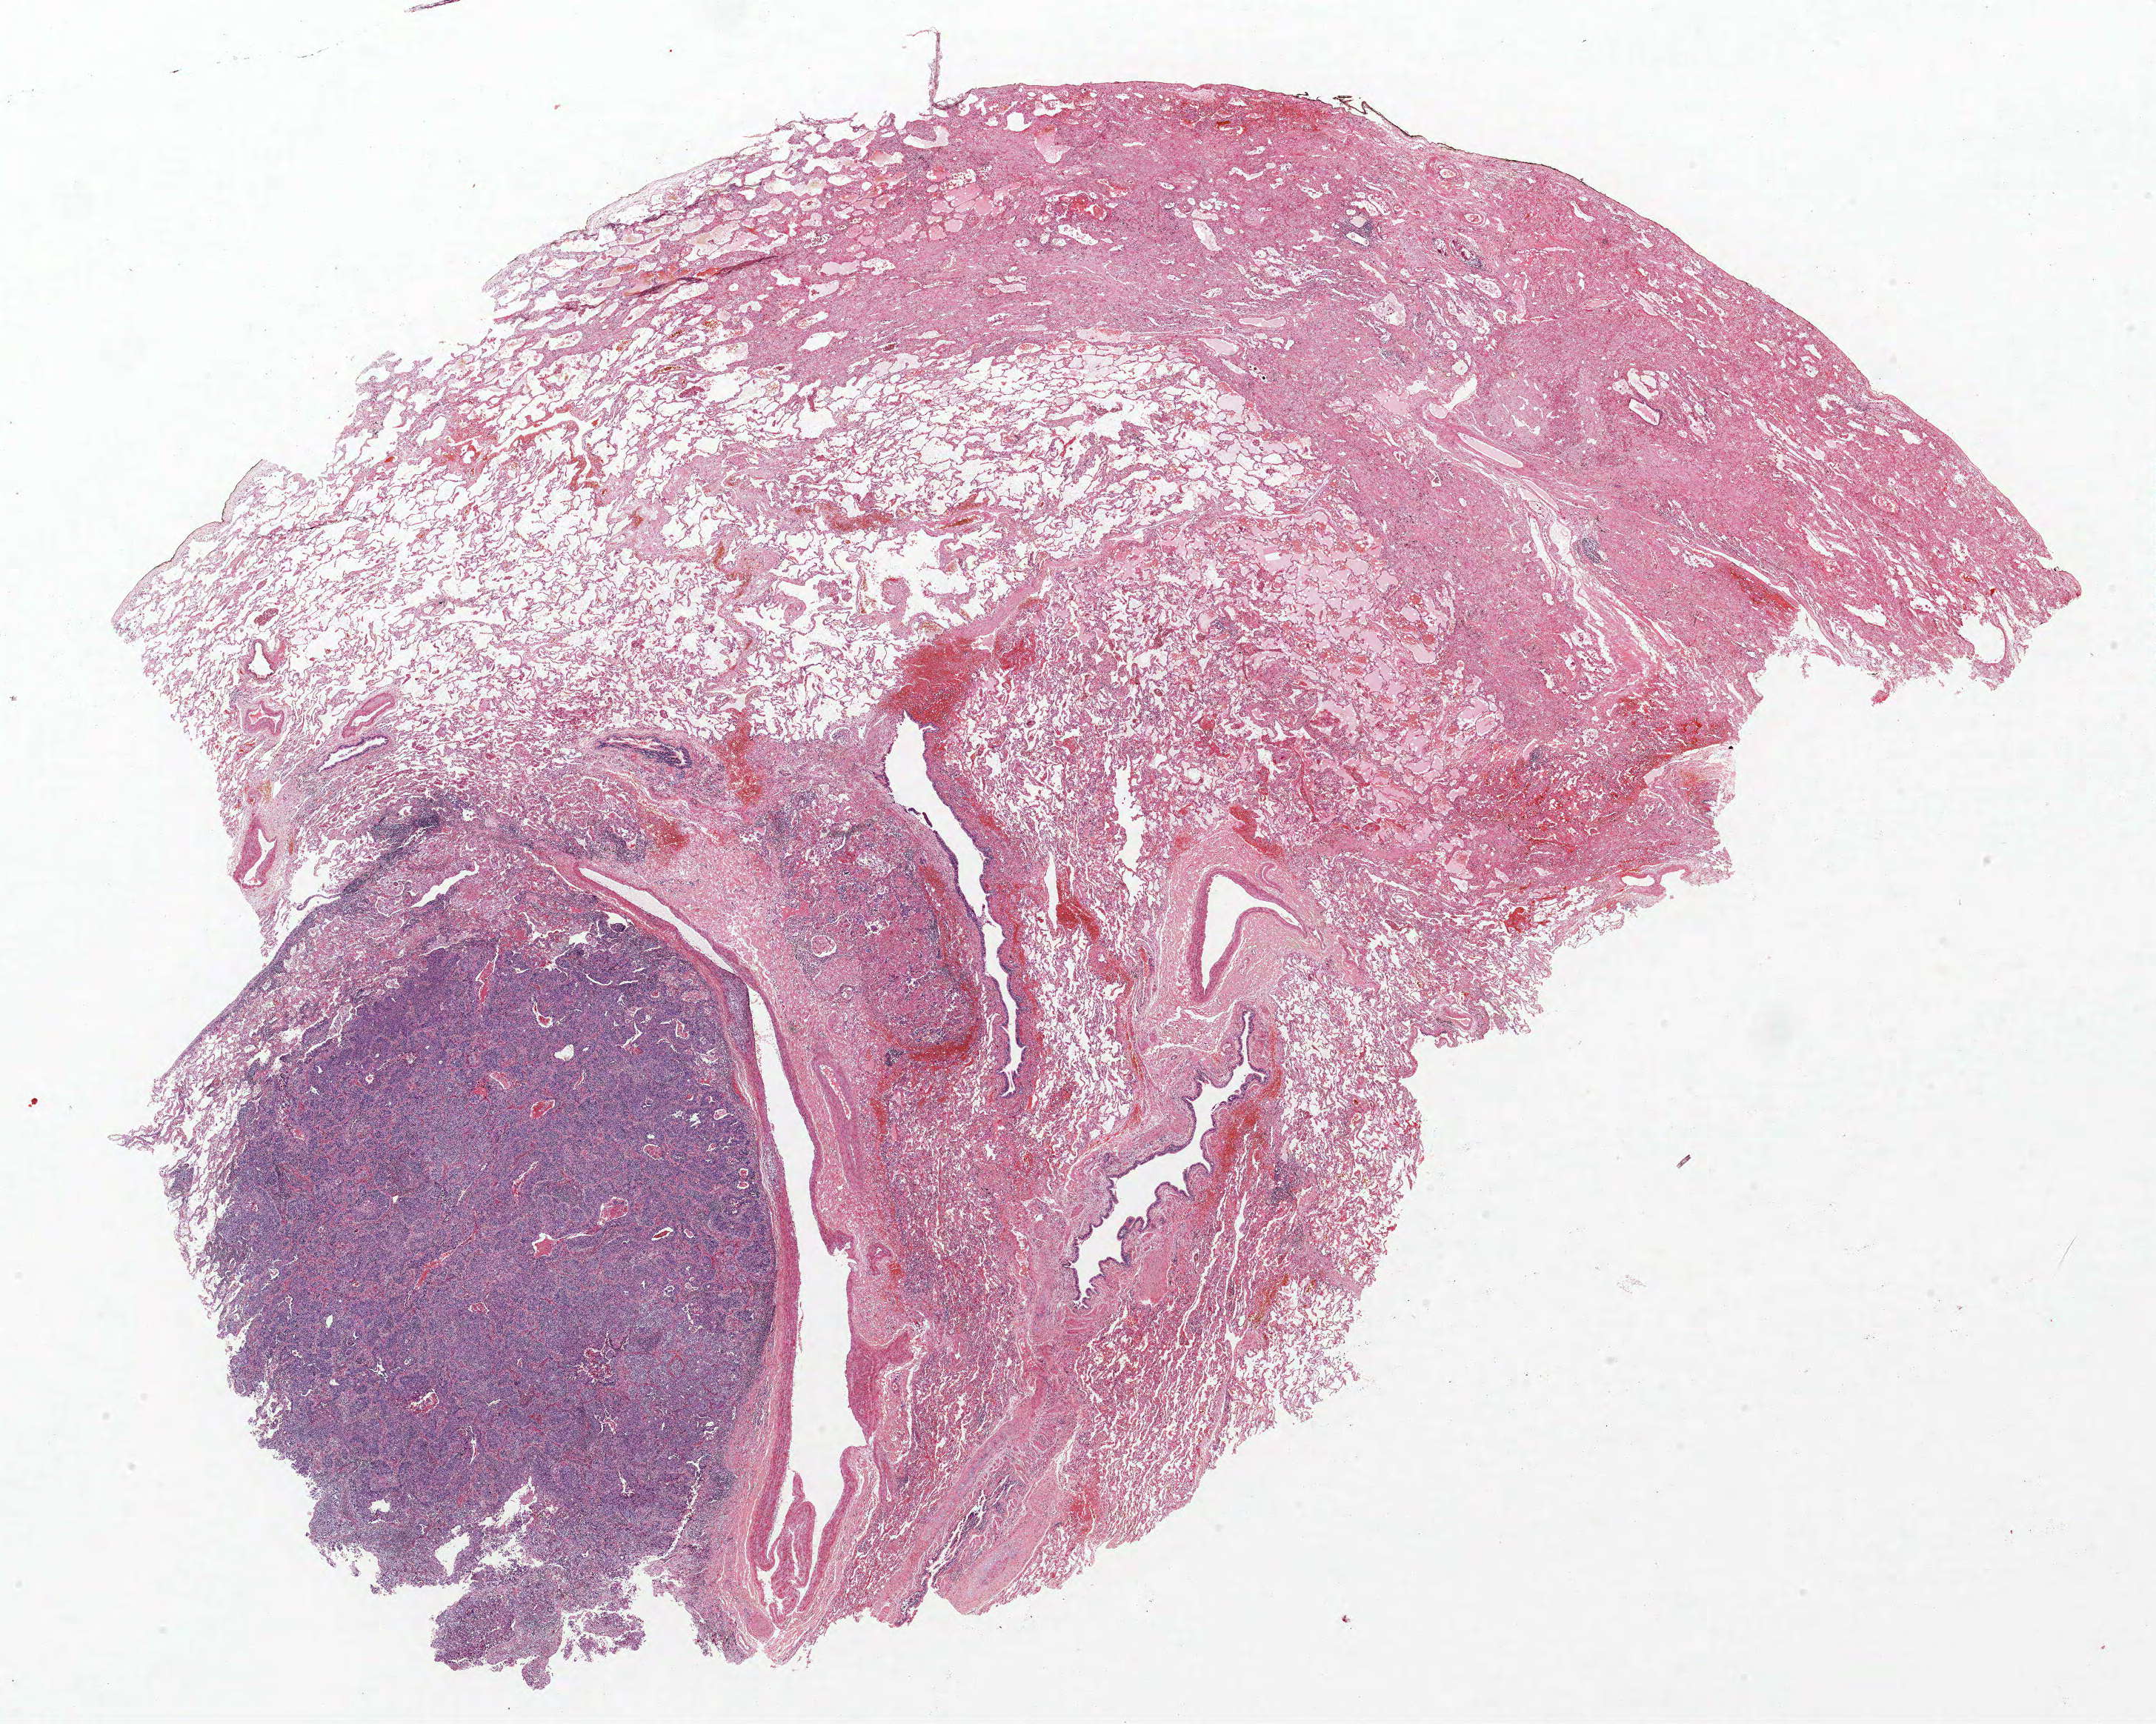
Whole-slide histology image, H&E-stained — whole scanned area (about 23.3 x 18.6 mm, slide scanned at 40x) shown as a low-resolution overview, formalin-fixed paraffin-embedded (FFPE) section, lung. Female patient, aged 56 at enrolment. Former smoker at enrolment. Grade: poorly differentiated (G3).
Tumour size (pathology): 11 mm. Stage (AJCC 6th edition): IA. Participant's lung-cancer diagnosis: Squamous cell carcinoma, NOS. Primary tumour location (clinical record): right upper lobe.